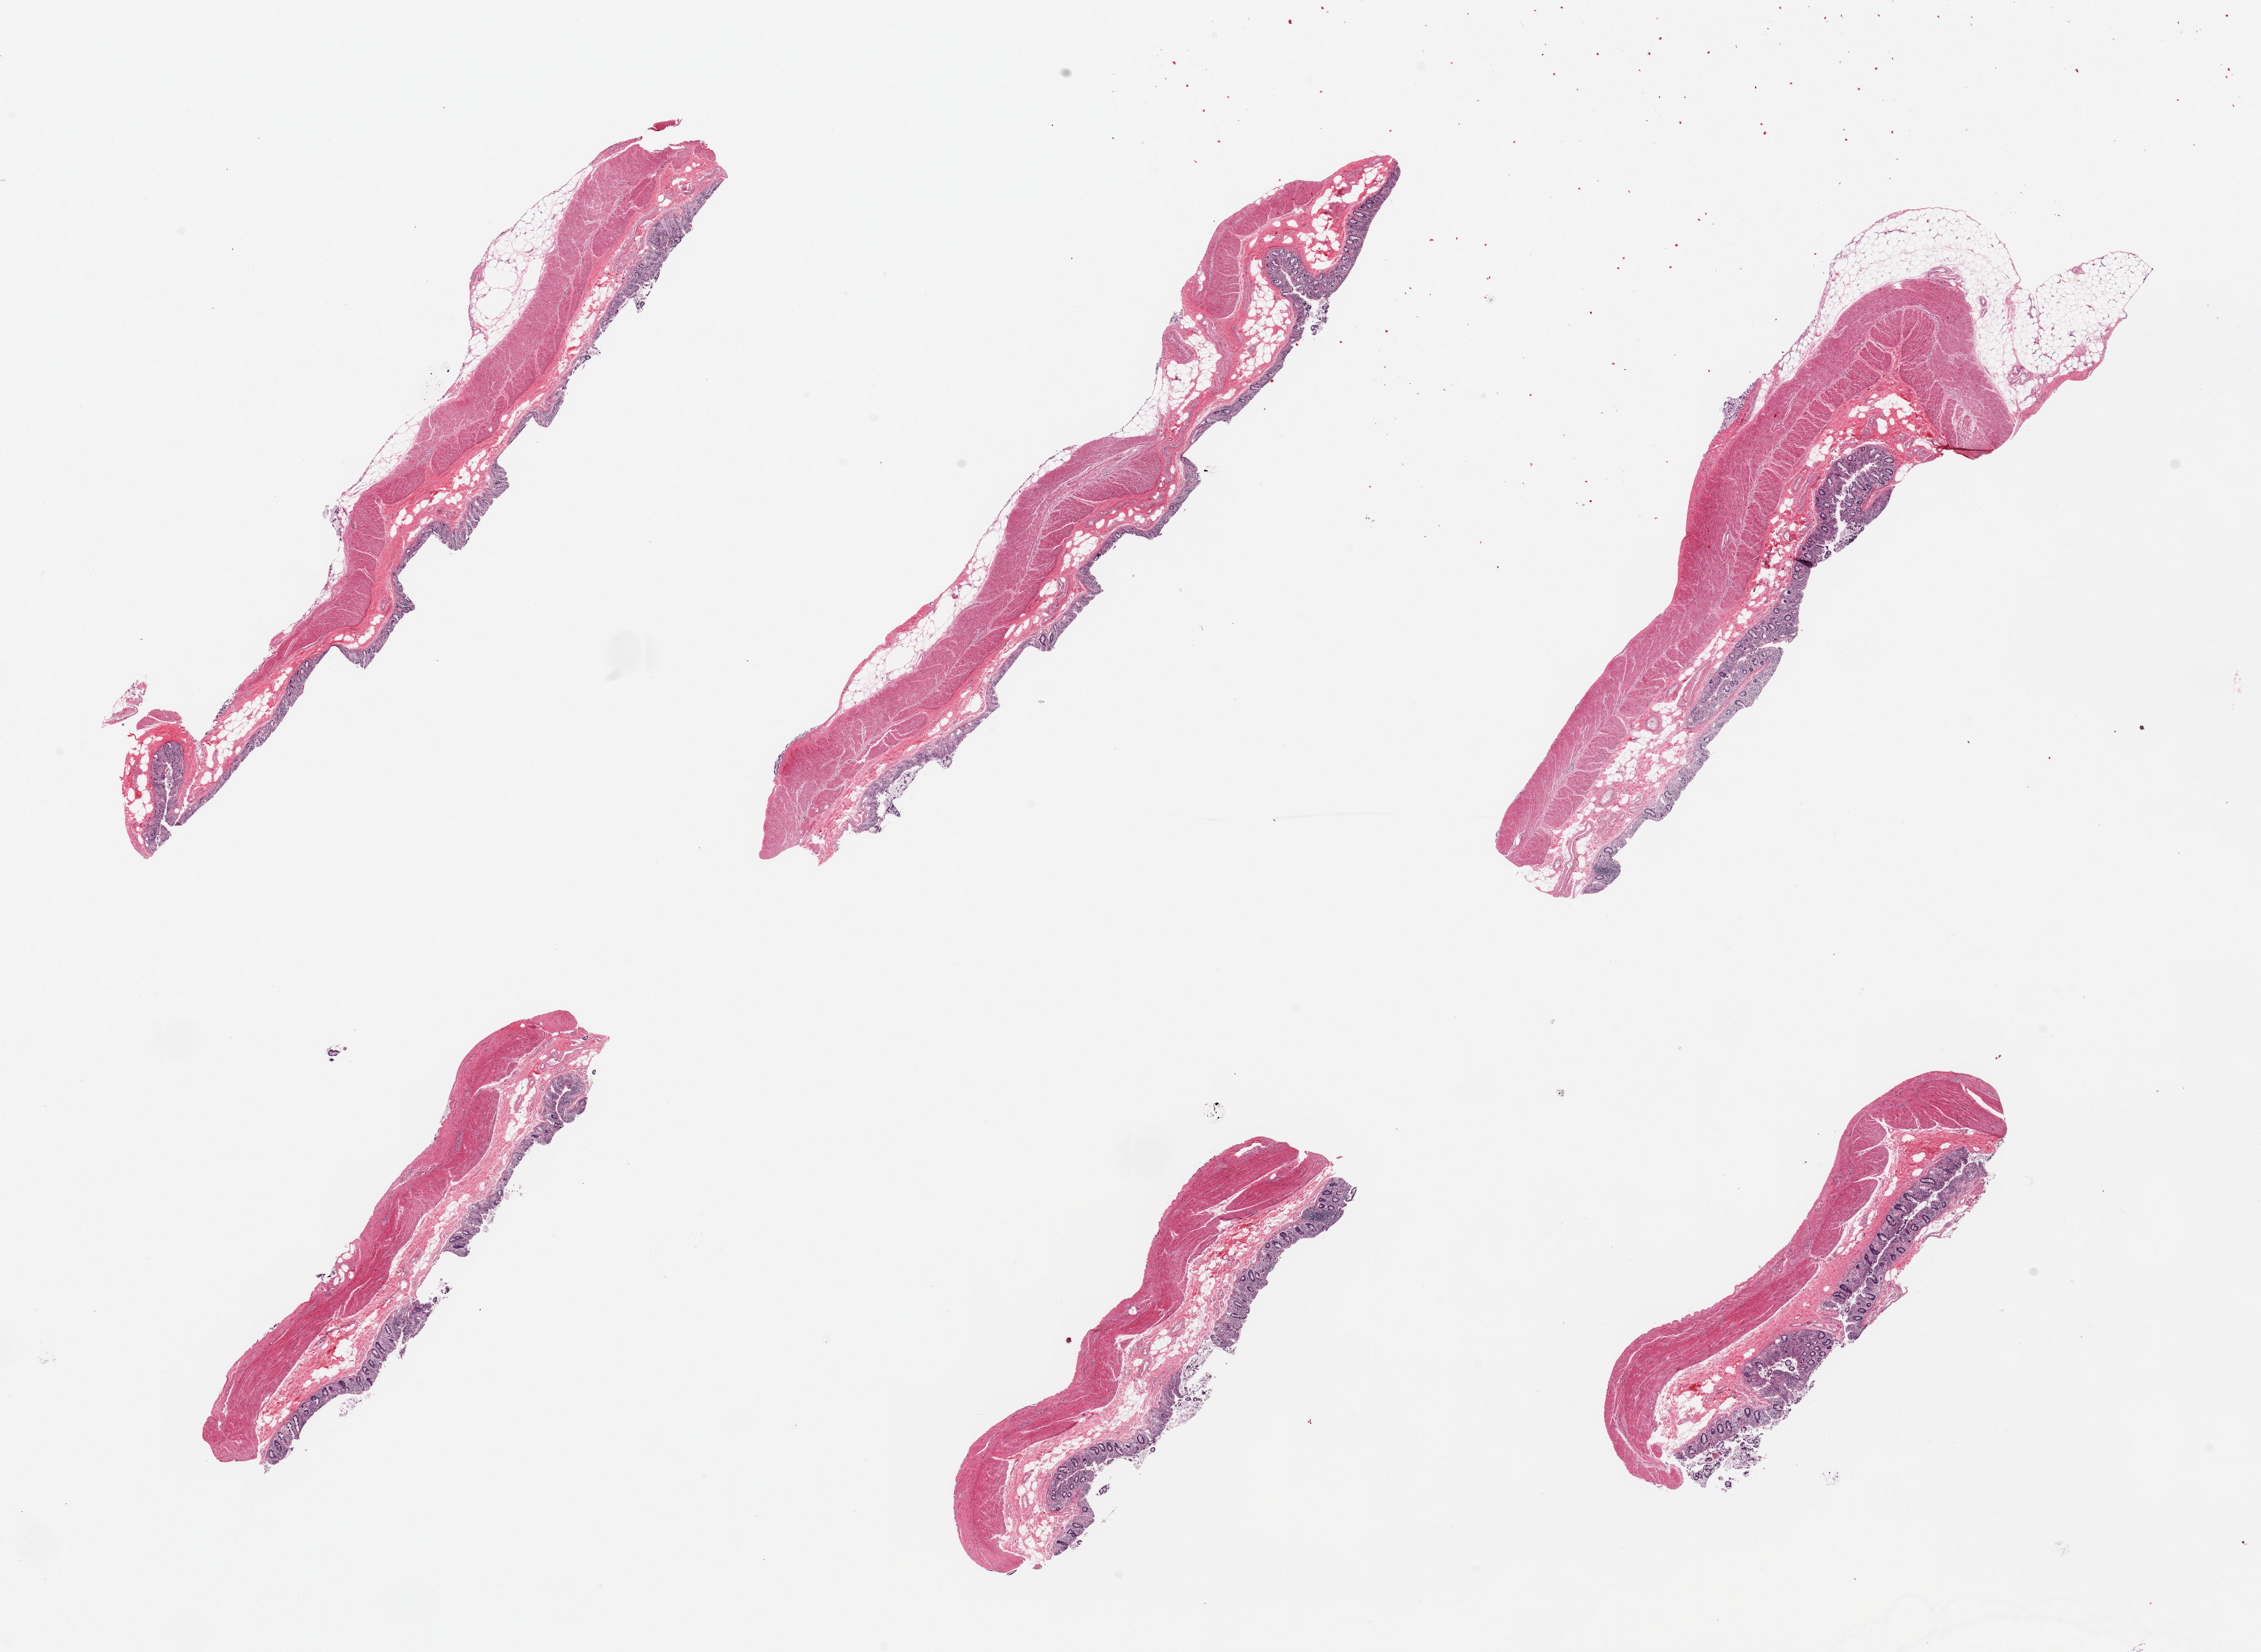
Digitized haematoxylin and eosin-stained section — low-resolution overview of the scanned area, about 27.6 x 20.1 mm; PAXgene-fixed paraffin-embedded (PFPE) section; target tissue: transverse colon; tissue donor sample.
* review note (as recorded): 6 pieces; full thickness sections